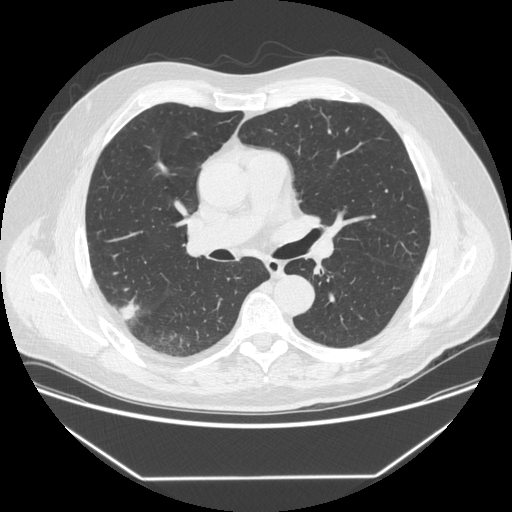
Low-dose screening chest CT, one axial slice. Slice 209 of 342 in the series (ordered by position). Lung window (W 1500 / L -600 HU). 1.25 mm slice thickness. 512 × 512 image matrix.
Annotated regions visible in this slice (outlined manually by an expert reader):
- lesion 1 (tumor, upper lobe of right lung): bounding box [x1, y1, x2, y2] px = [120, 301, 140, 321]